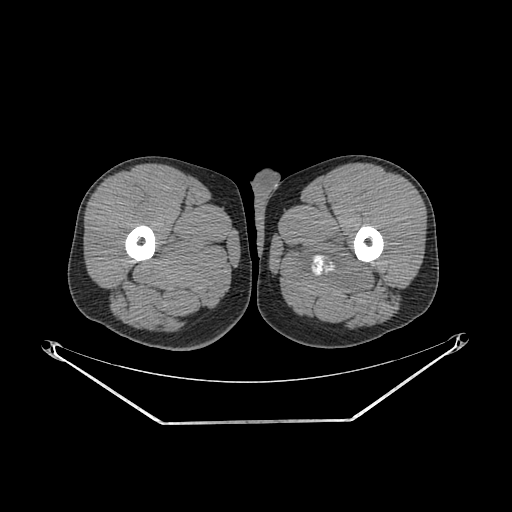
CT of an extremity soft-tissue mass (from a PET/CT study), one axial slice. Position 250 of 267 along the scan axis. Reconstruction kernel SOFT. Soft-tissue window (W 400 / L 40 HU). 3.75 mm slice thickness. 512 × 512 image matrix, field of view 500 × 500 mm. Male patient. From the clinical record (not read from this slice): histological type: extraskeletal osteosarcoma; grade: high; site of the primary tumour: left adductur.
Annotated regions visible in this slice (expert contour drawn on MRI and transferred to this co-registered scan by the dataset authors):
- gross tumour volume (mass): bounding box (x1, y1, x2, y2) in pixels: (288, 228, 378, 296)